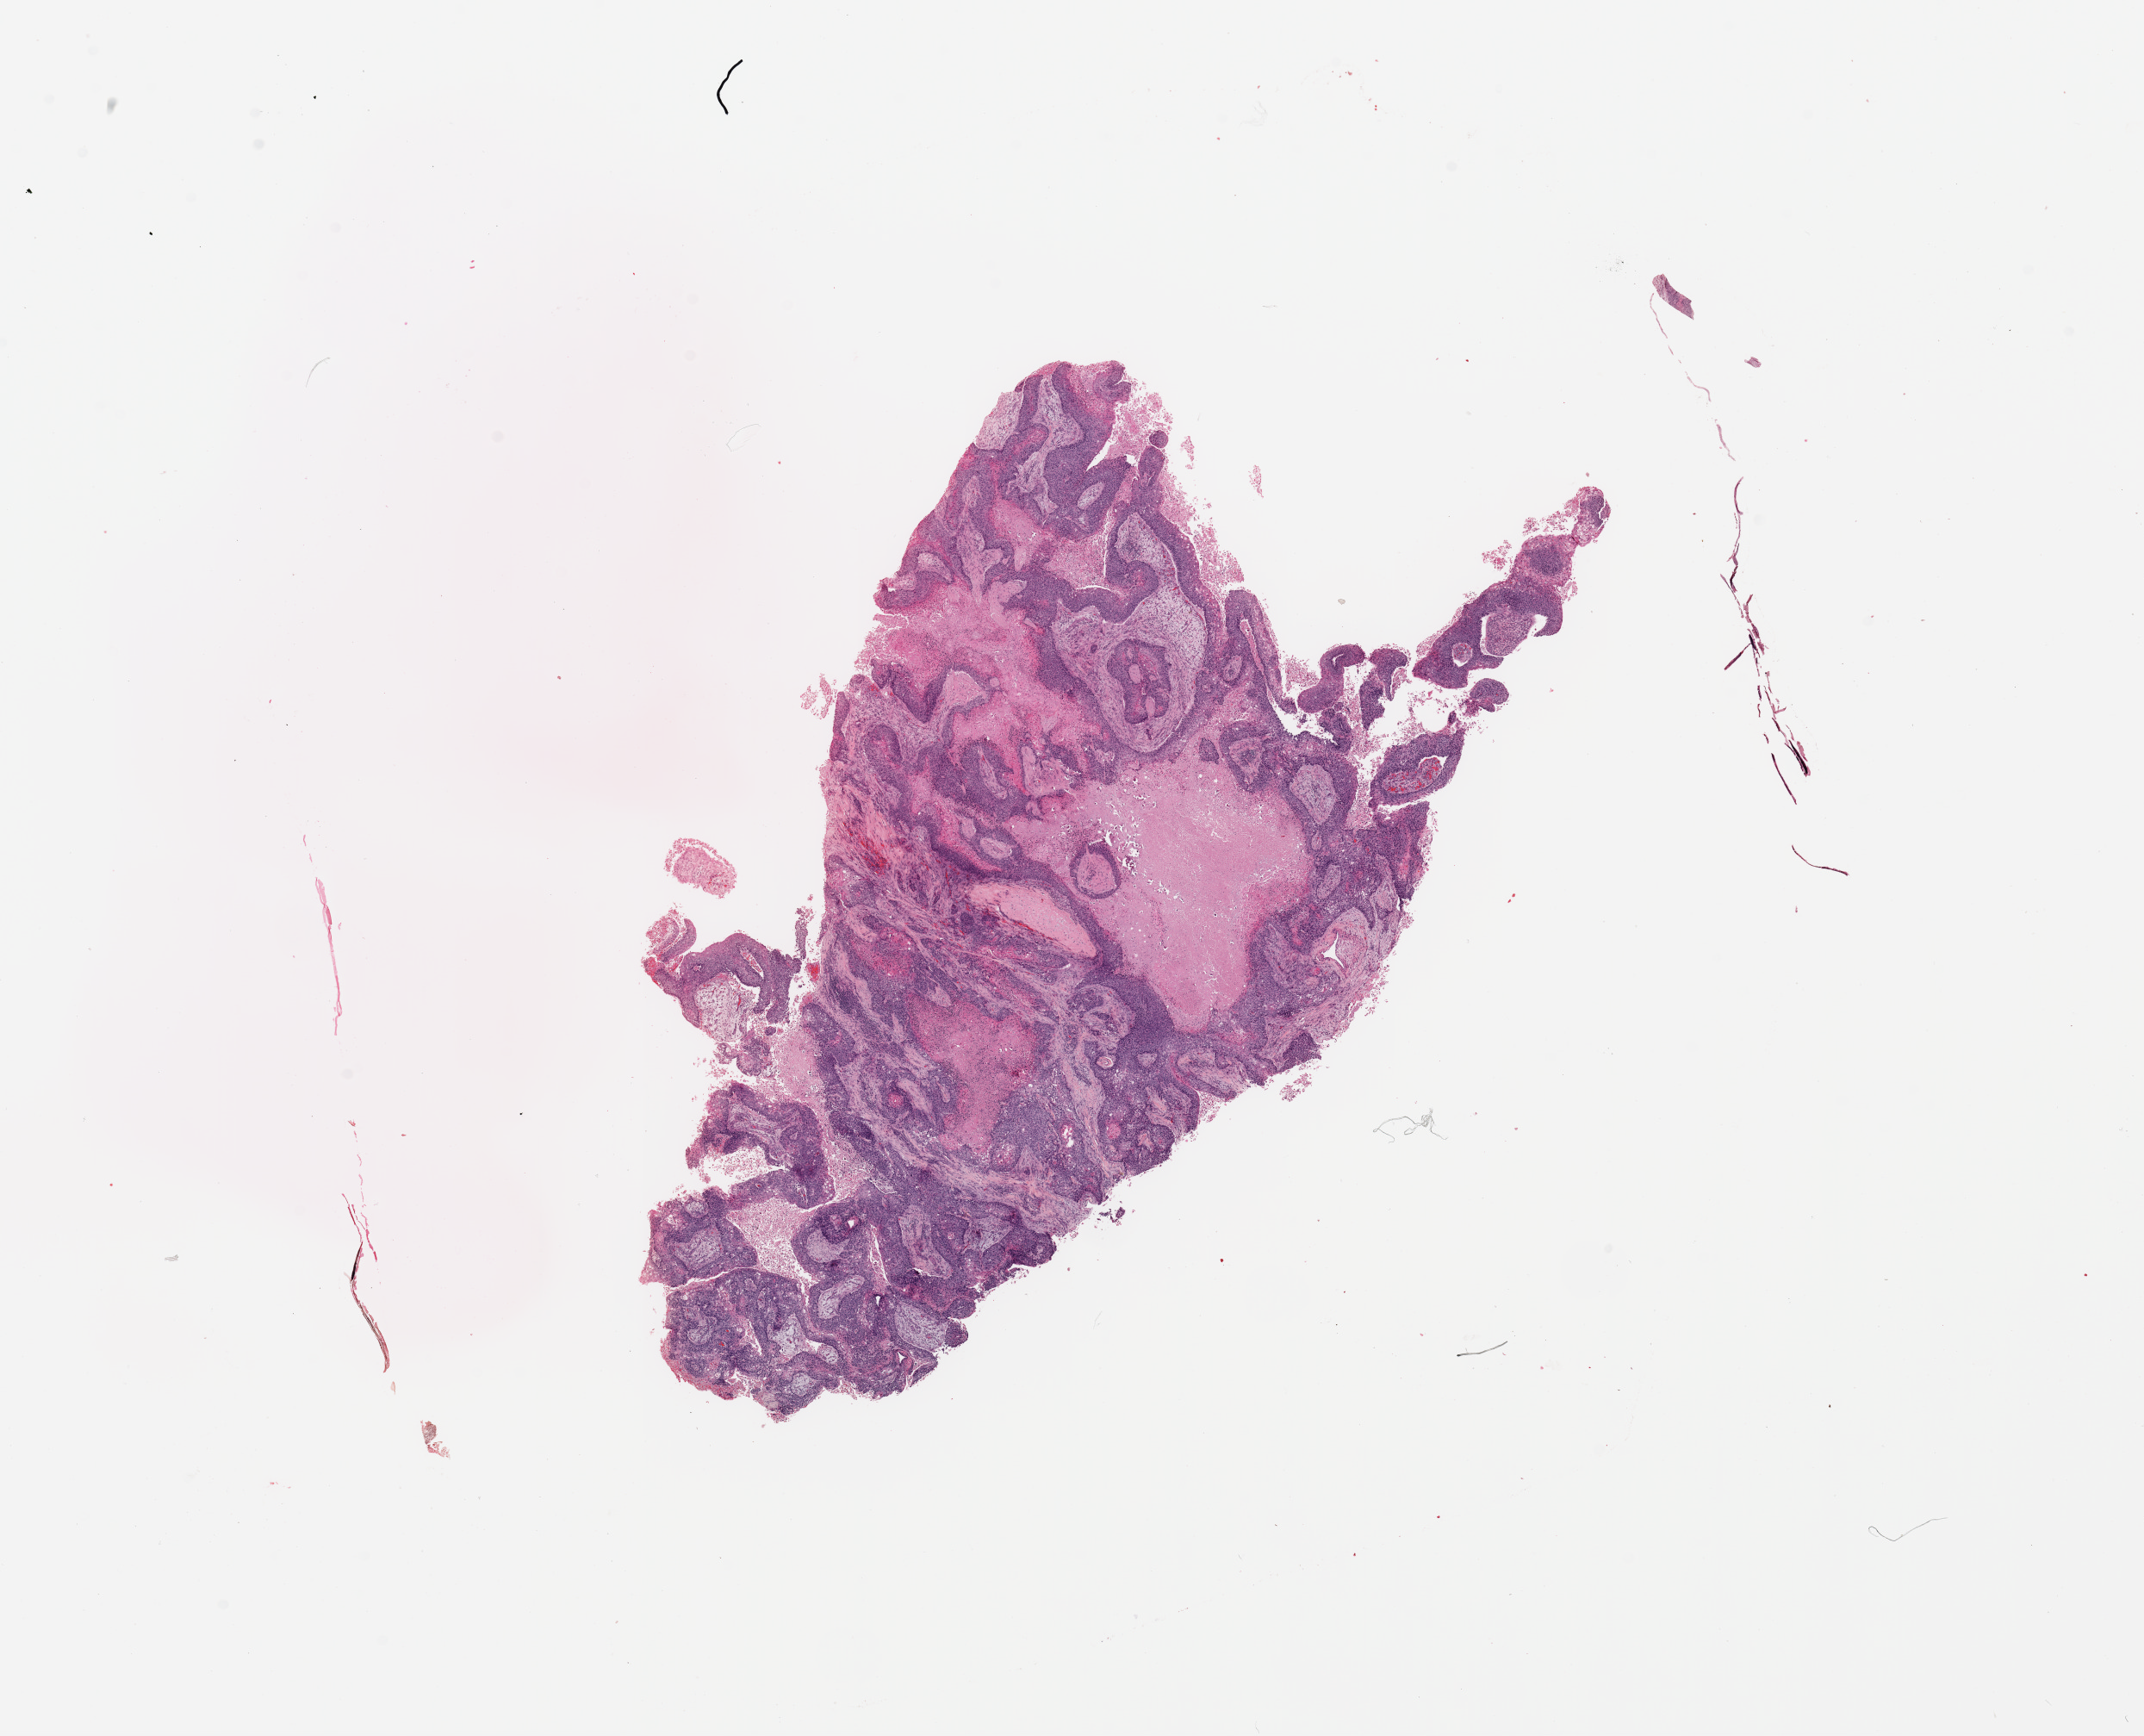
Digitized H&E tissue section (whole slide), a low-resolution overview of the entire scanned area, about 19.7 x 15.9 mm (acquisition: 20x scan), tumour tissue sample, sampled site: lung. Patient: male, age 78 years. Histologic grade: G2 (moderately differentiated). Pathologist review of this section (percent, as recorded): tumour nuclei 70%, necrosis 15%.
AJCC pathologic stage: III. Diagnosis: Squamous cell carcinoma, NOS. Primary tumour site (as recorded): right middle lobe.